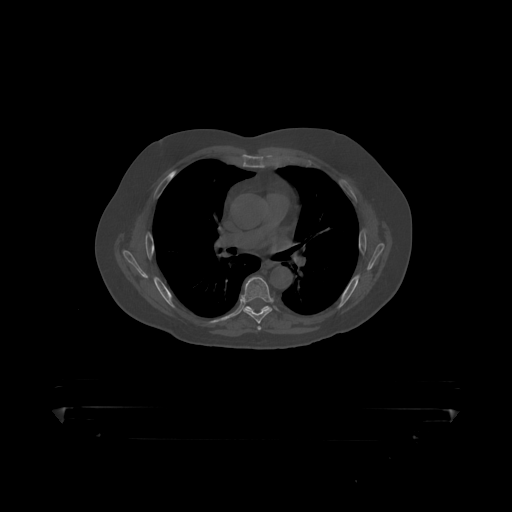
CT including the spine, one axial slice. Position 296 of 390 along the scan axis. Reconstruction kernel STANDARD. 120 kVp. Bone window (W 1800 / L 400 HU). 1.25 mm slice thickness. 512 × 512 image matrix, field of view 650 × 650 mm. Patient: male, 60 years. Case-level facts recorded for this patient, not image findings: primary cancer: prostate.
Annotated regions visible in this slice (semi-automatic segmentation, software-assisted and operator-edited):
- T6 vertebra: bounding box [x1, y1, x2, y2] px = [241, 277, 273, 319]
- T7 vertebra: [245, 306, 270, 311]